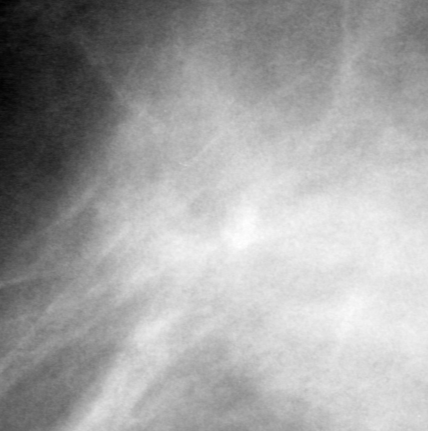
Crop from a digitized film mammogram around one marked abnormality, right breast, MLO view, BI-RADS breast density category 1 (scale 1–4).
- Marked abnormality: mass, shape oval, margins obscured; BI-RADS assessment category 0 (incomplete: needs additional imaging); pathology result (as recorded, not read from the image): benign.